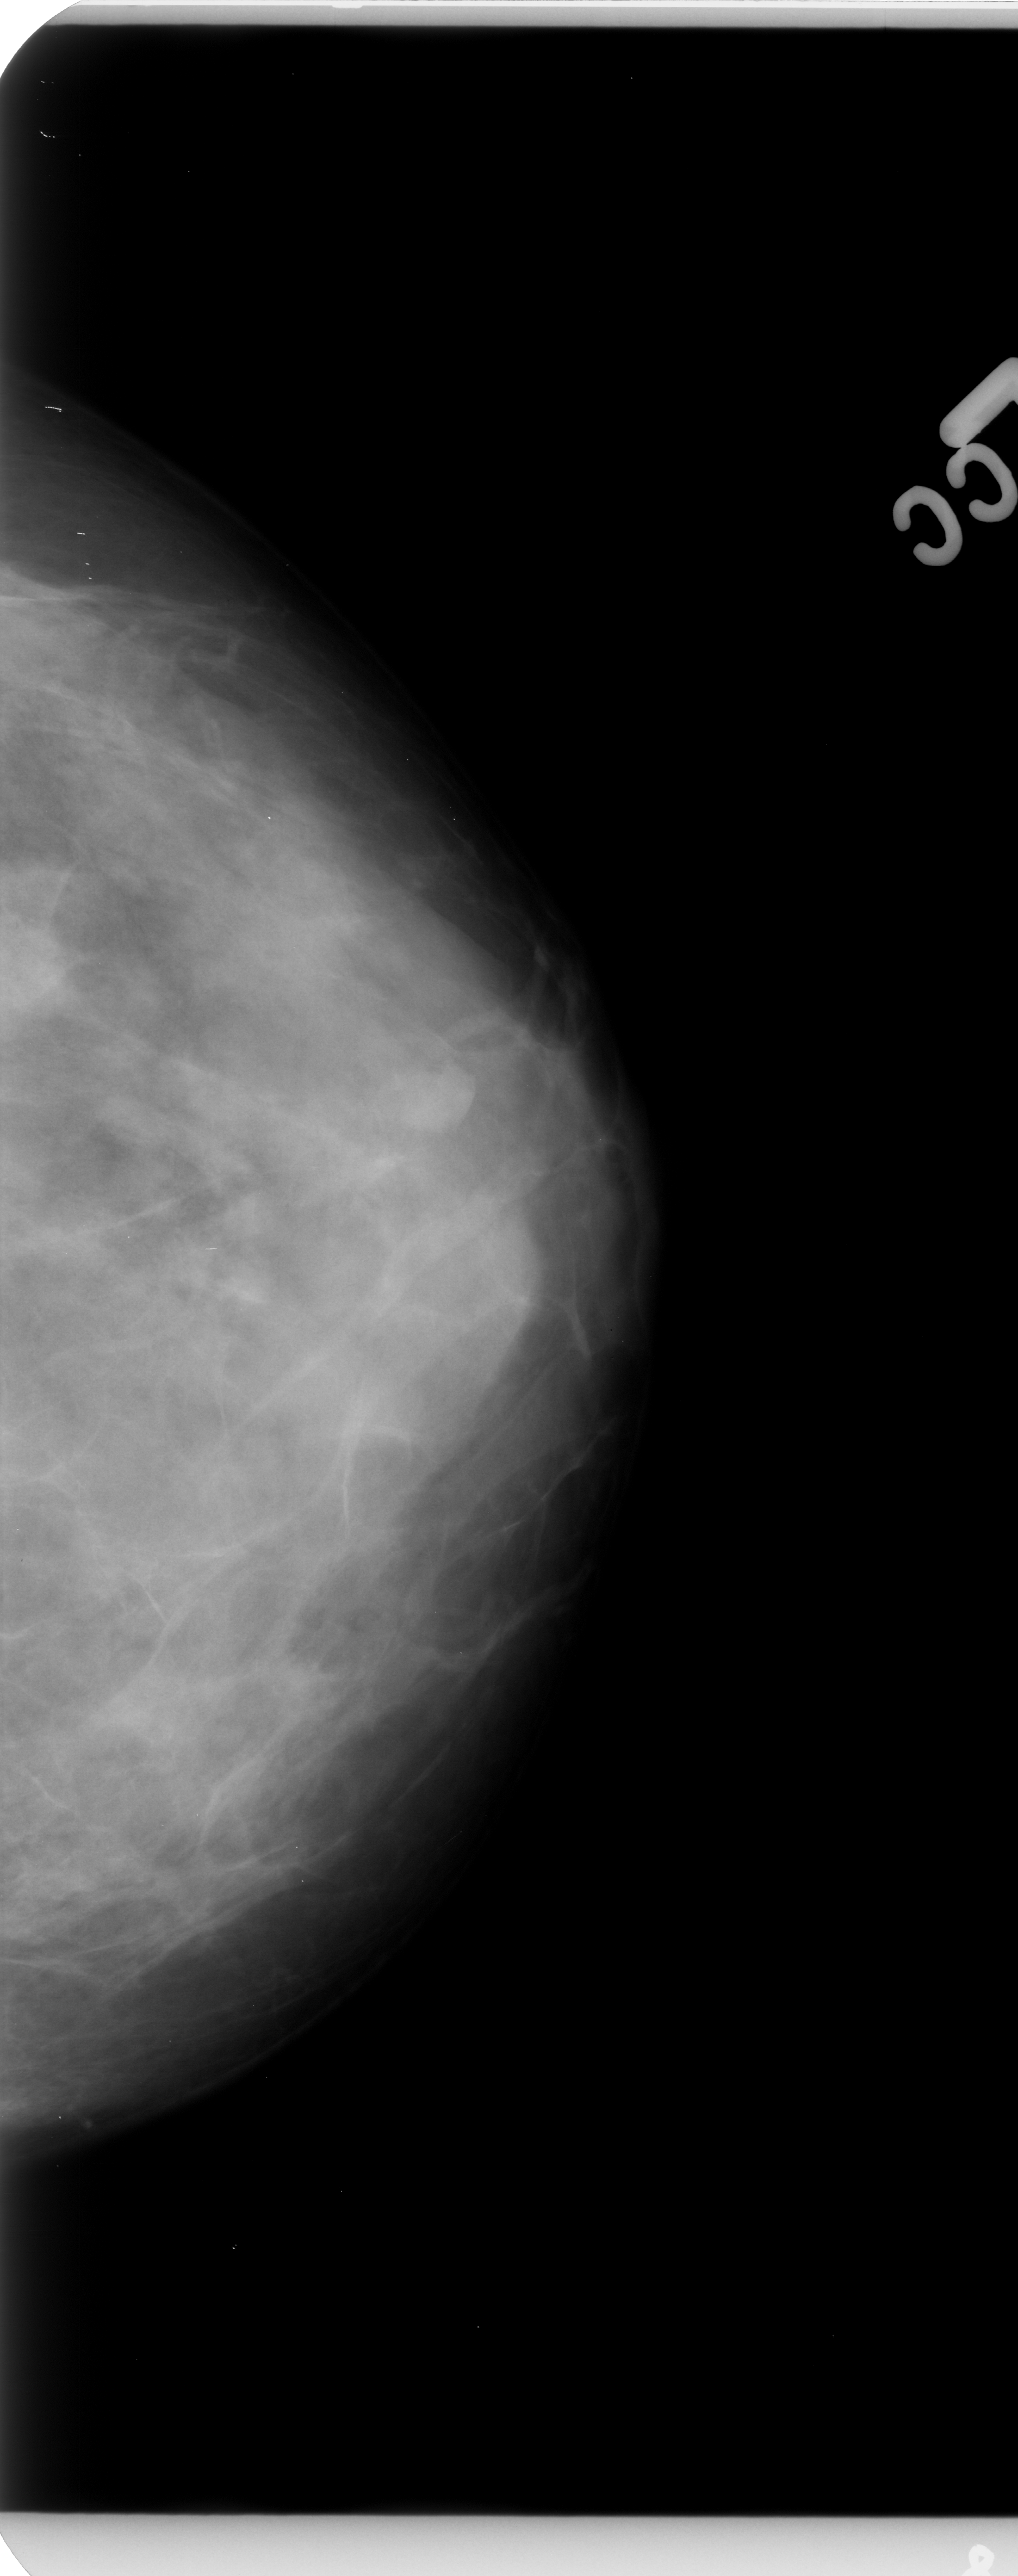
Digitized screen-film mammogram, left breast, craniocaudal (CC) view, breast composition: extremely dense (BI-RADS density category 4 of 4).
Mass, shape irregular, margins circumscribed / obscured; BI-RADS assessment category 4; pathology (as recorded): benign.